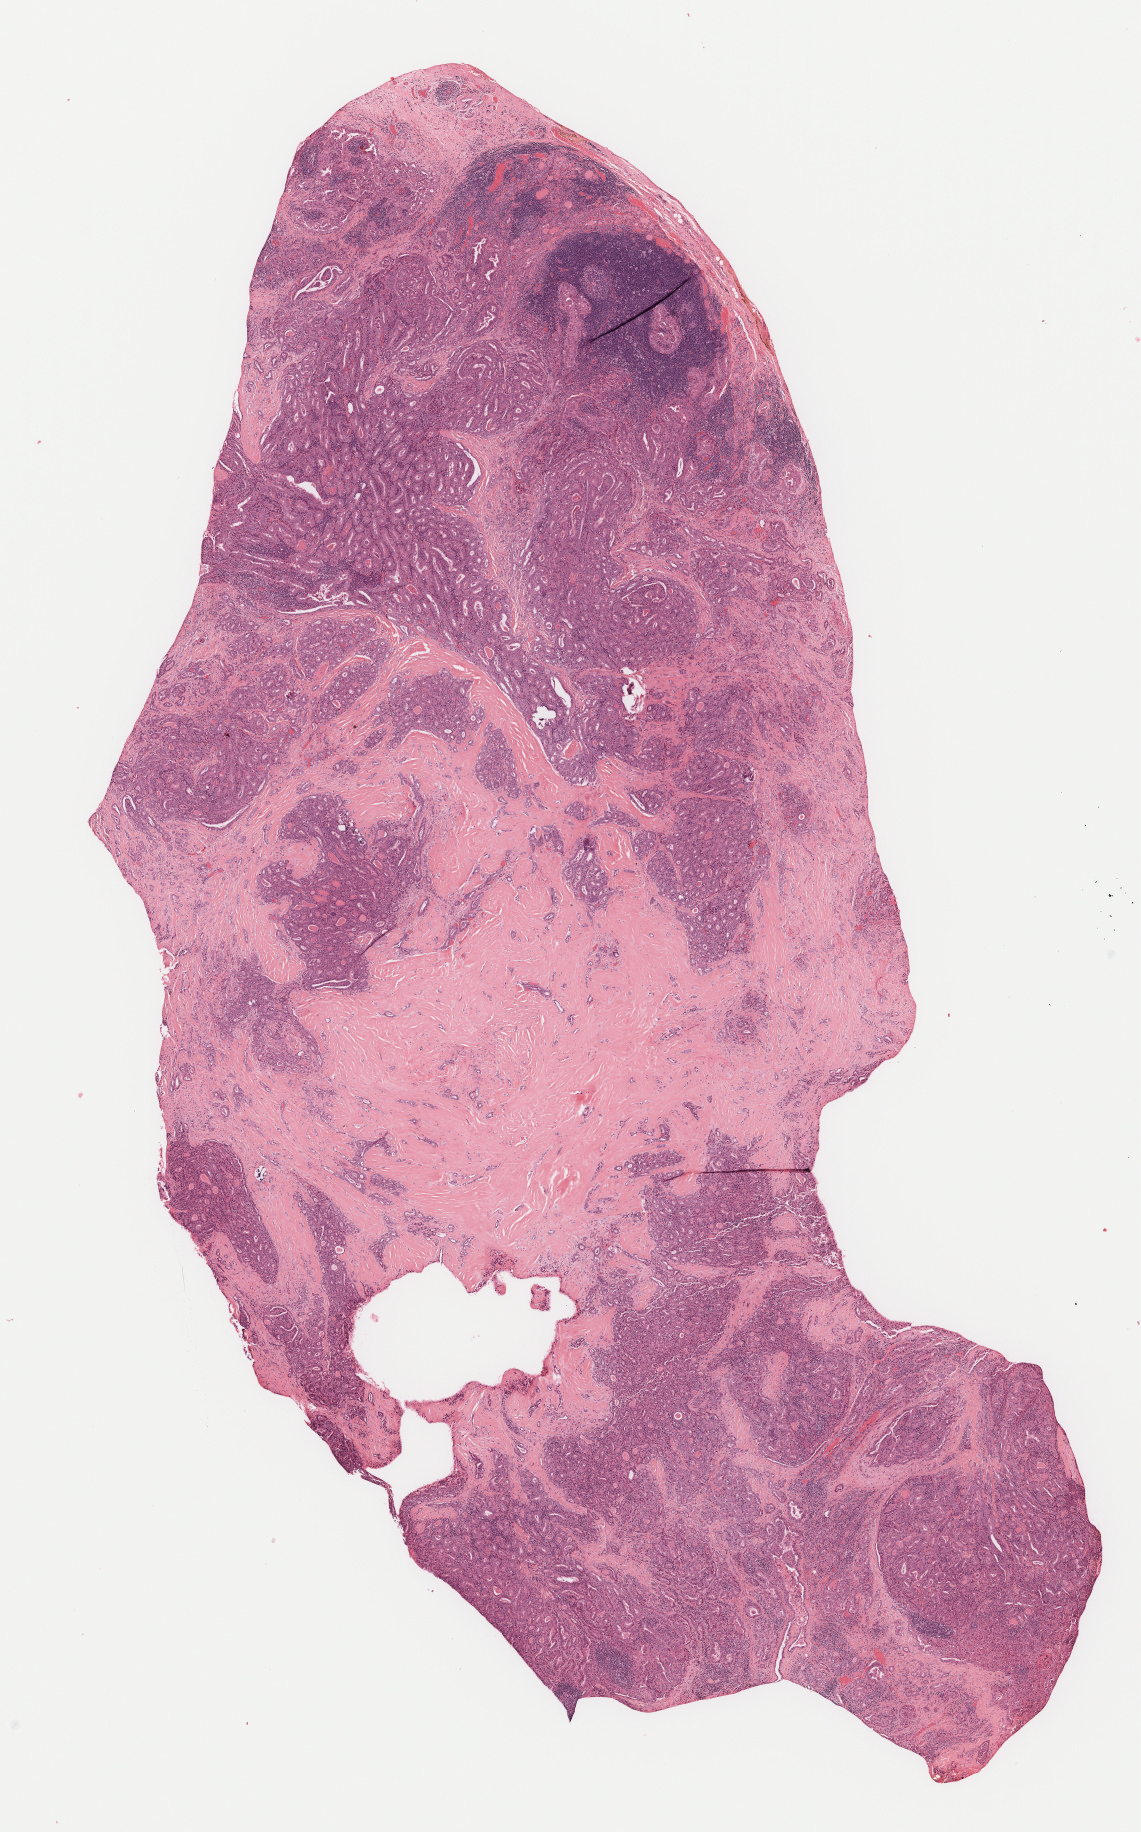
Digitized H&E tissue section (whole slide), low-resolution overview of the scanned area, about 9.2 x 14.8 mm; formalin-fixed paraffin-embedded (FFPE) diagnostic section; sample: primary tumour, thyroid. Male, age 33 years at initial diagnosis.
Histologic diagnosis: Papillary adenocarcinoma, NOS (thyroid gland). AJCC pathologic stage: I (7th edition). Lymph nodes positive (case pathology): 15 of 54 examined.